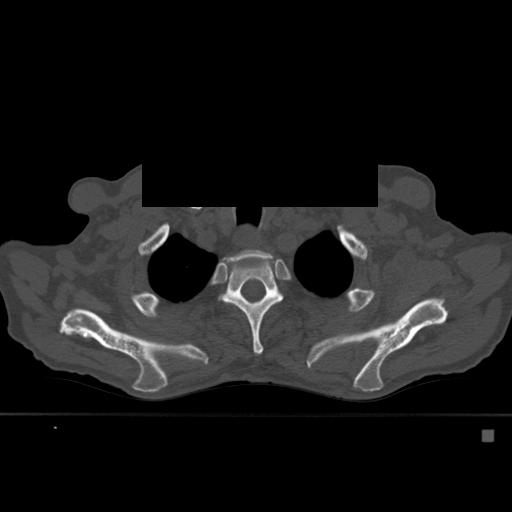
CT including the spine, one axial slice. Slice 433 of 527 in the series (ordered by position). Bone window (W 1800 / L 400 HU). 1.5 mm slice thickness. 512 × 512 image matrix, field of view 373 × 373 mm. Male patient, age 78 years. Case-level facts recorded for this patient, not image findings: primary cancer: prostate.
Structures marked on this image (semi-automatically segmented with operator editing):
- T2 vertebra: bounding box (x1, y1, x2, y2) in pixels: (229, 250, 272, 260)
- T3 vertebra: (221, 258, 283, 356)